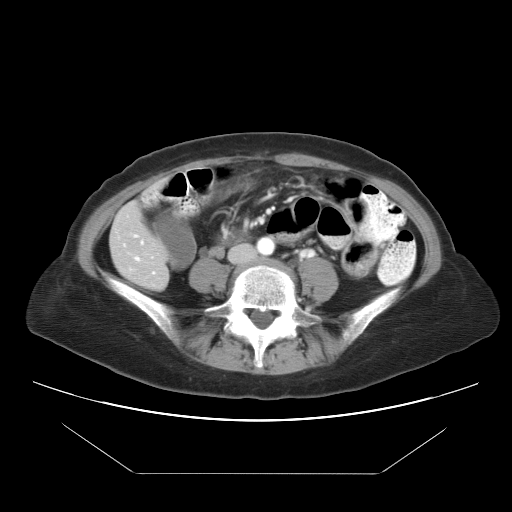
Contrast-enhanced abdominal CT, one axial slice. Reconstruction kernel STANDARD. 120 kVp. Intravenous contrast given. Soft-tissue window (W 400 / L 40 HU). 7.5 mm slice thickness. 512 × 512 image matrix, field of view 392 × 392 mm. Female patient, age 72 years. From the clinical record (not read from this slice): diagnosis: colorectal cancer liver metastases, imaged before liver resection.
Annotated regions visible in this slice (expert manual segmentation):
- hepatic veins: bounding box <136,241,143,260> (left, top, right, bottom; pixels)
- liver: <111,204,170,292>
- planned liver remnant (the part of the liver to remain after resection): <111,203,169,292>